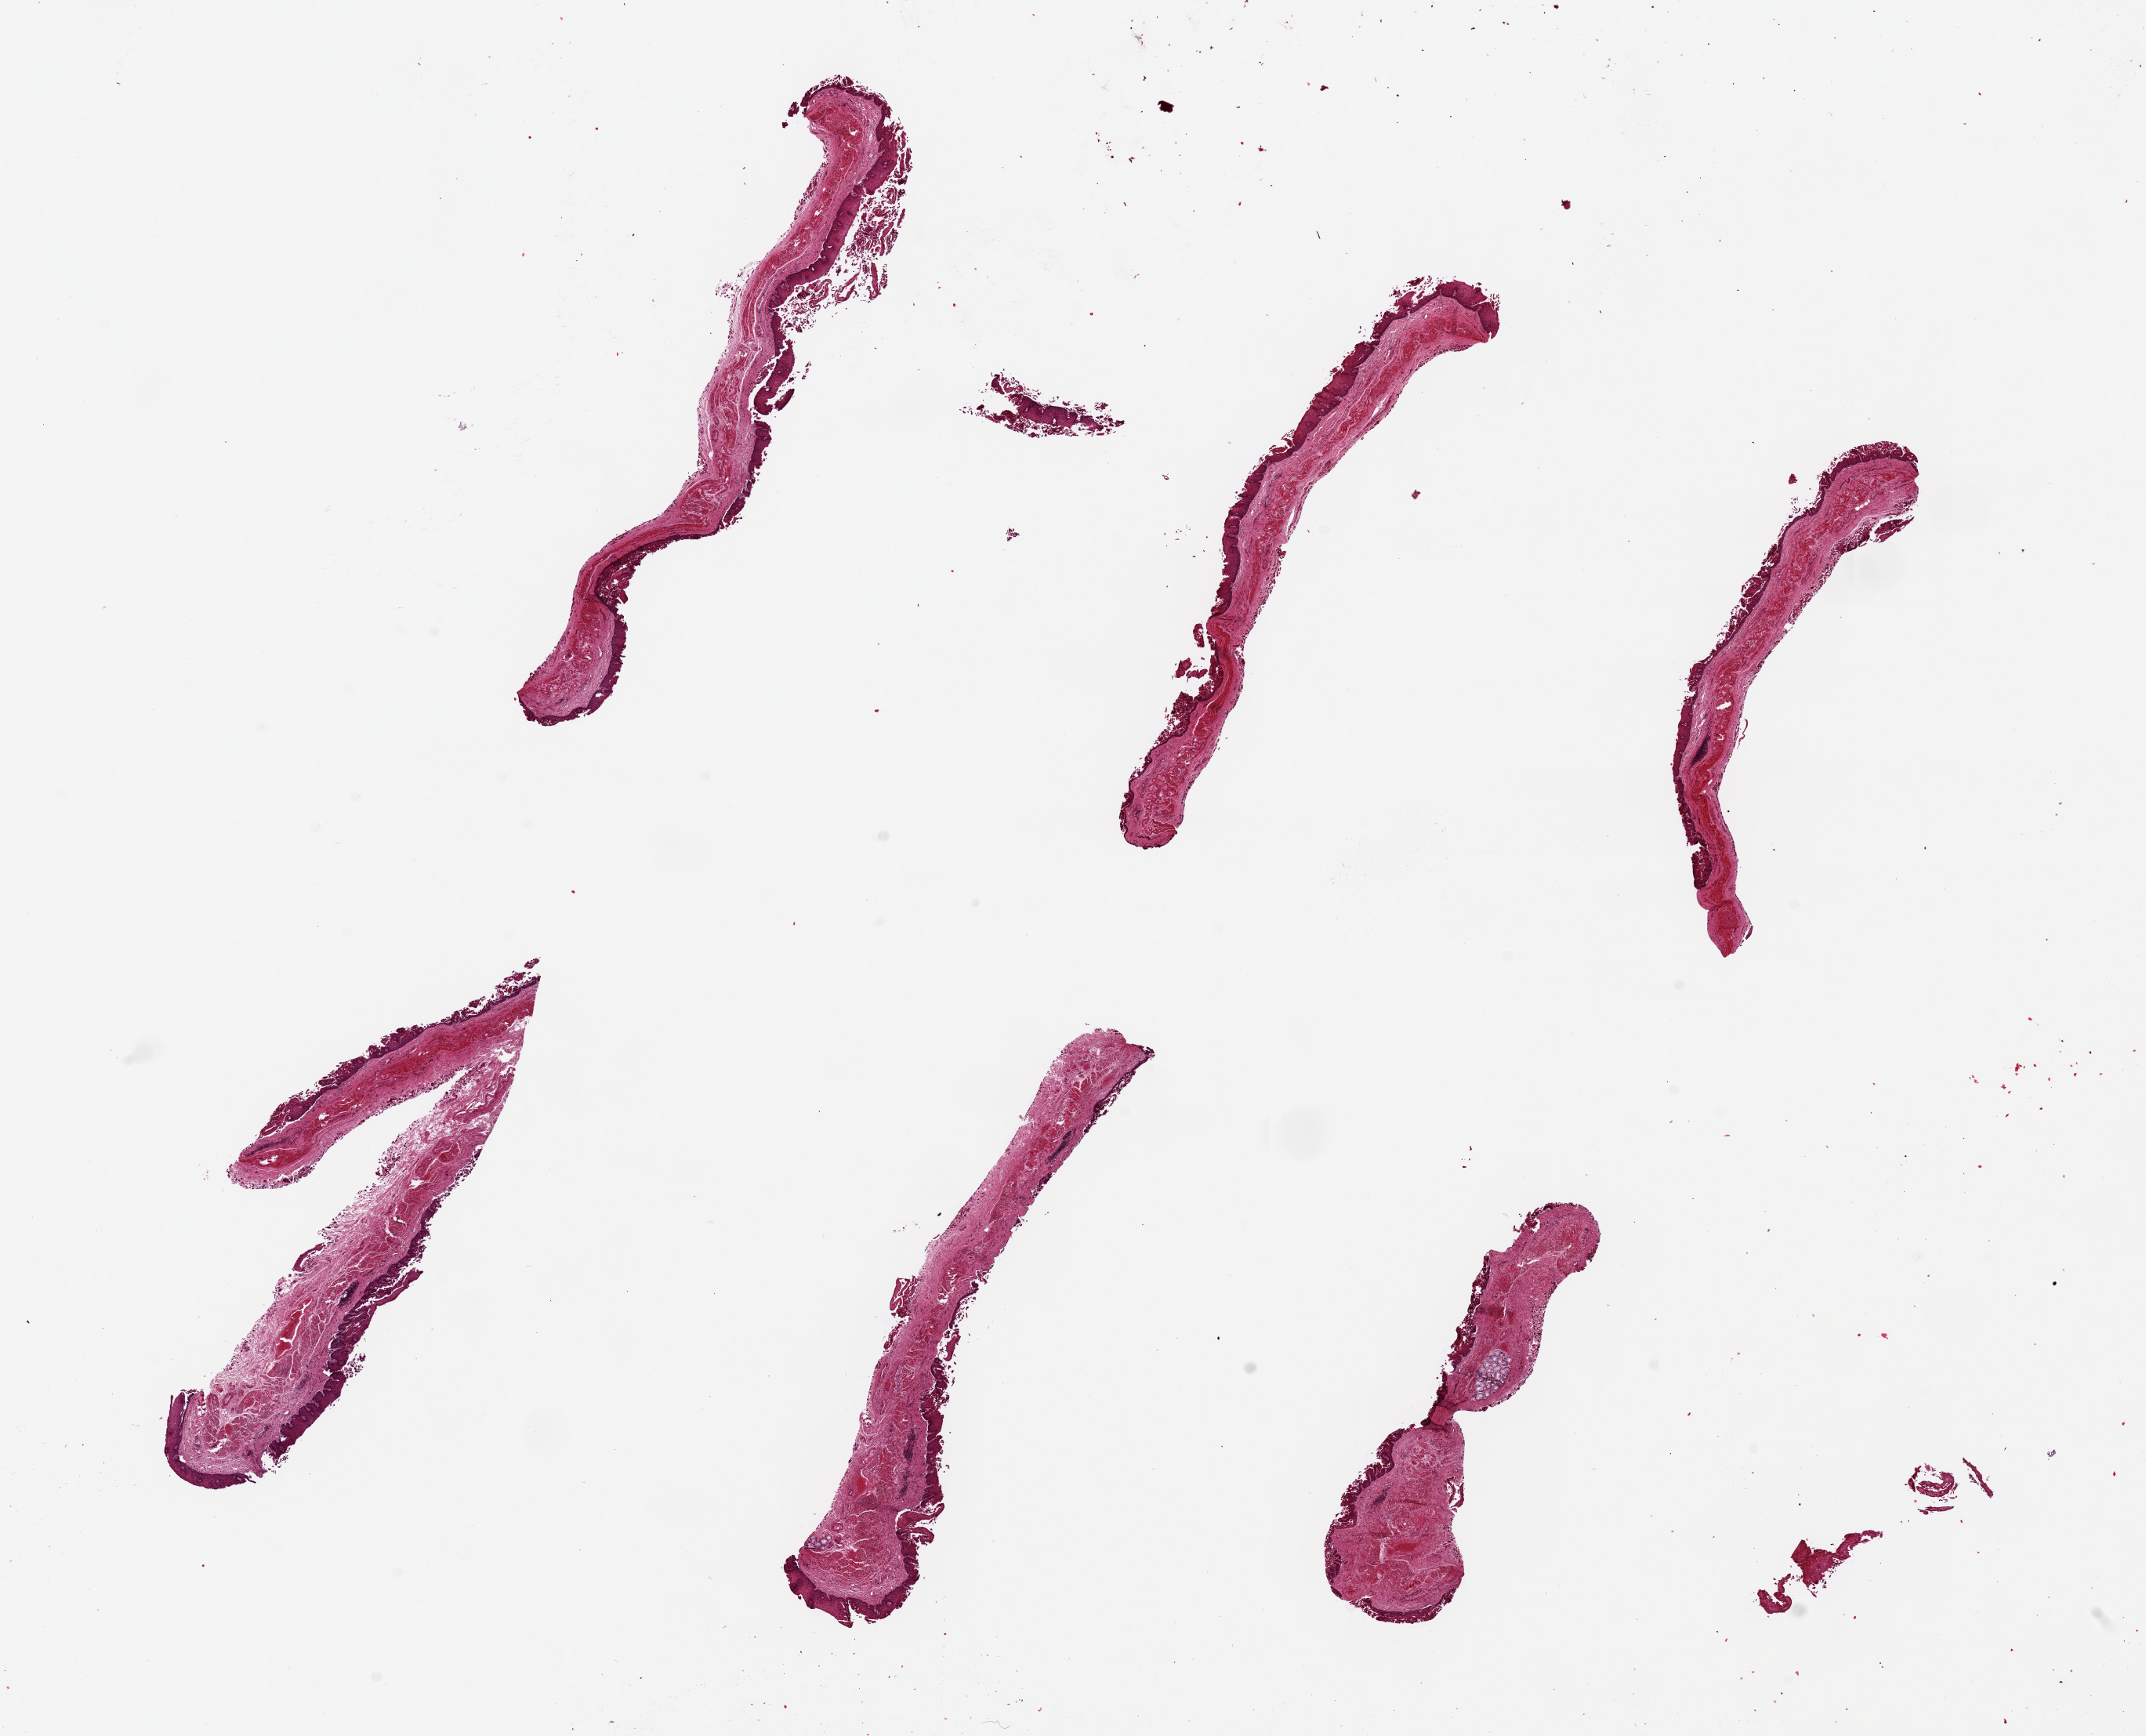
Whole-slide image, haematoxylin and eosin stain, a low-resolution overview of the entire scanned area, about 21.7 x 17.5 mm (slide scanned at 20x); PAXgene-fixed, paraffin-embedded tissue; target tissue: esophageal mucous membrane; donor tissue sample.
• reviewer comment on this tissue sample: 6 pieces ~7x0.5mm, squamous mucosa 10-30% of thickness, unusually poorly preserved